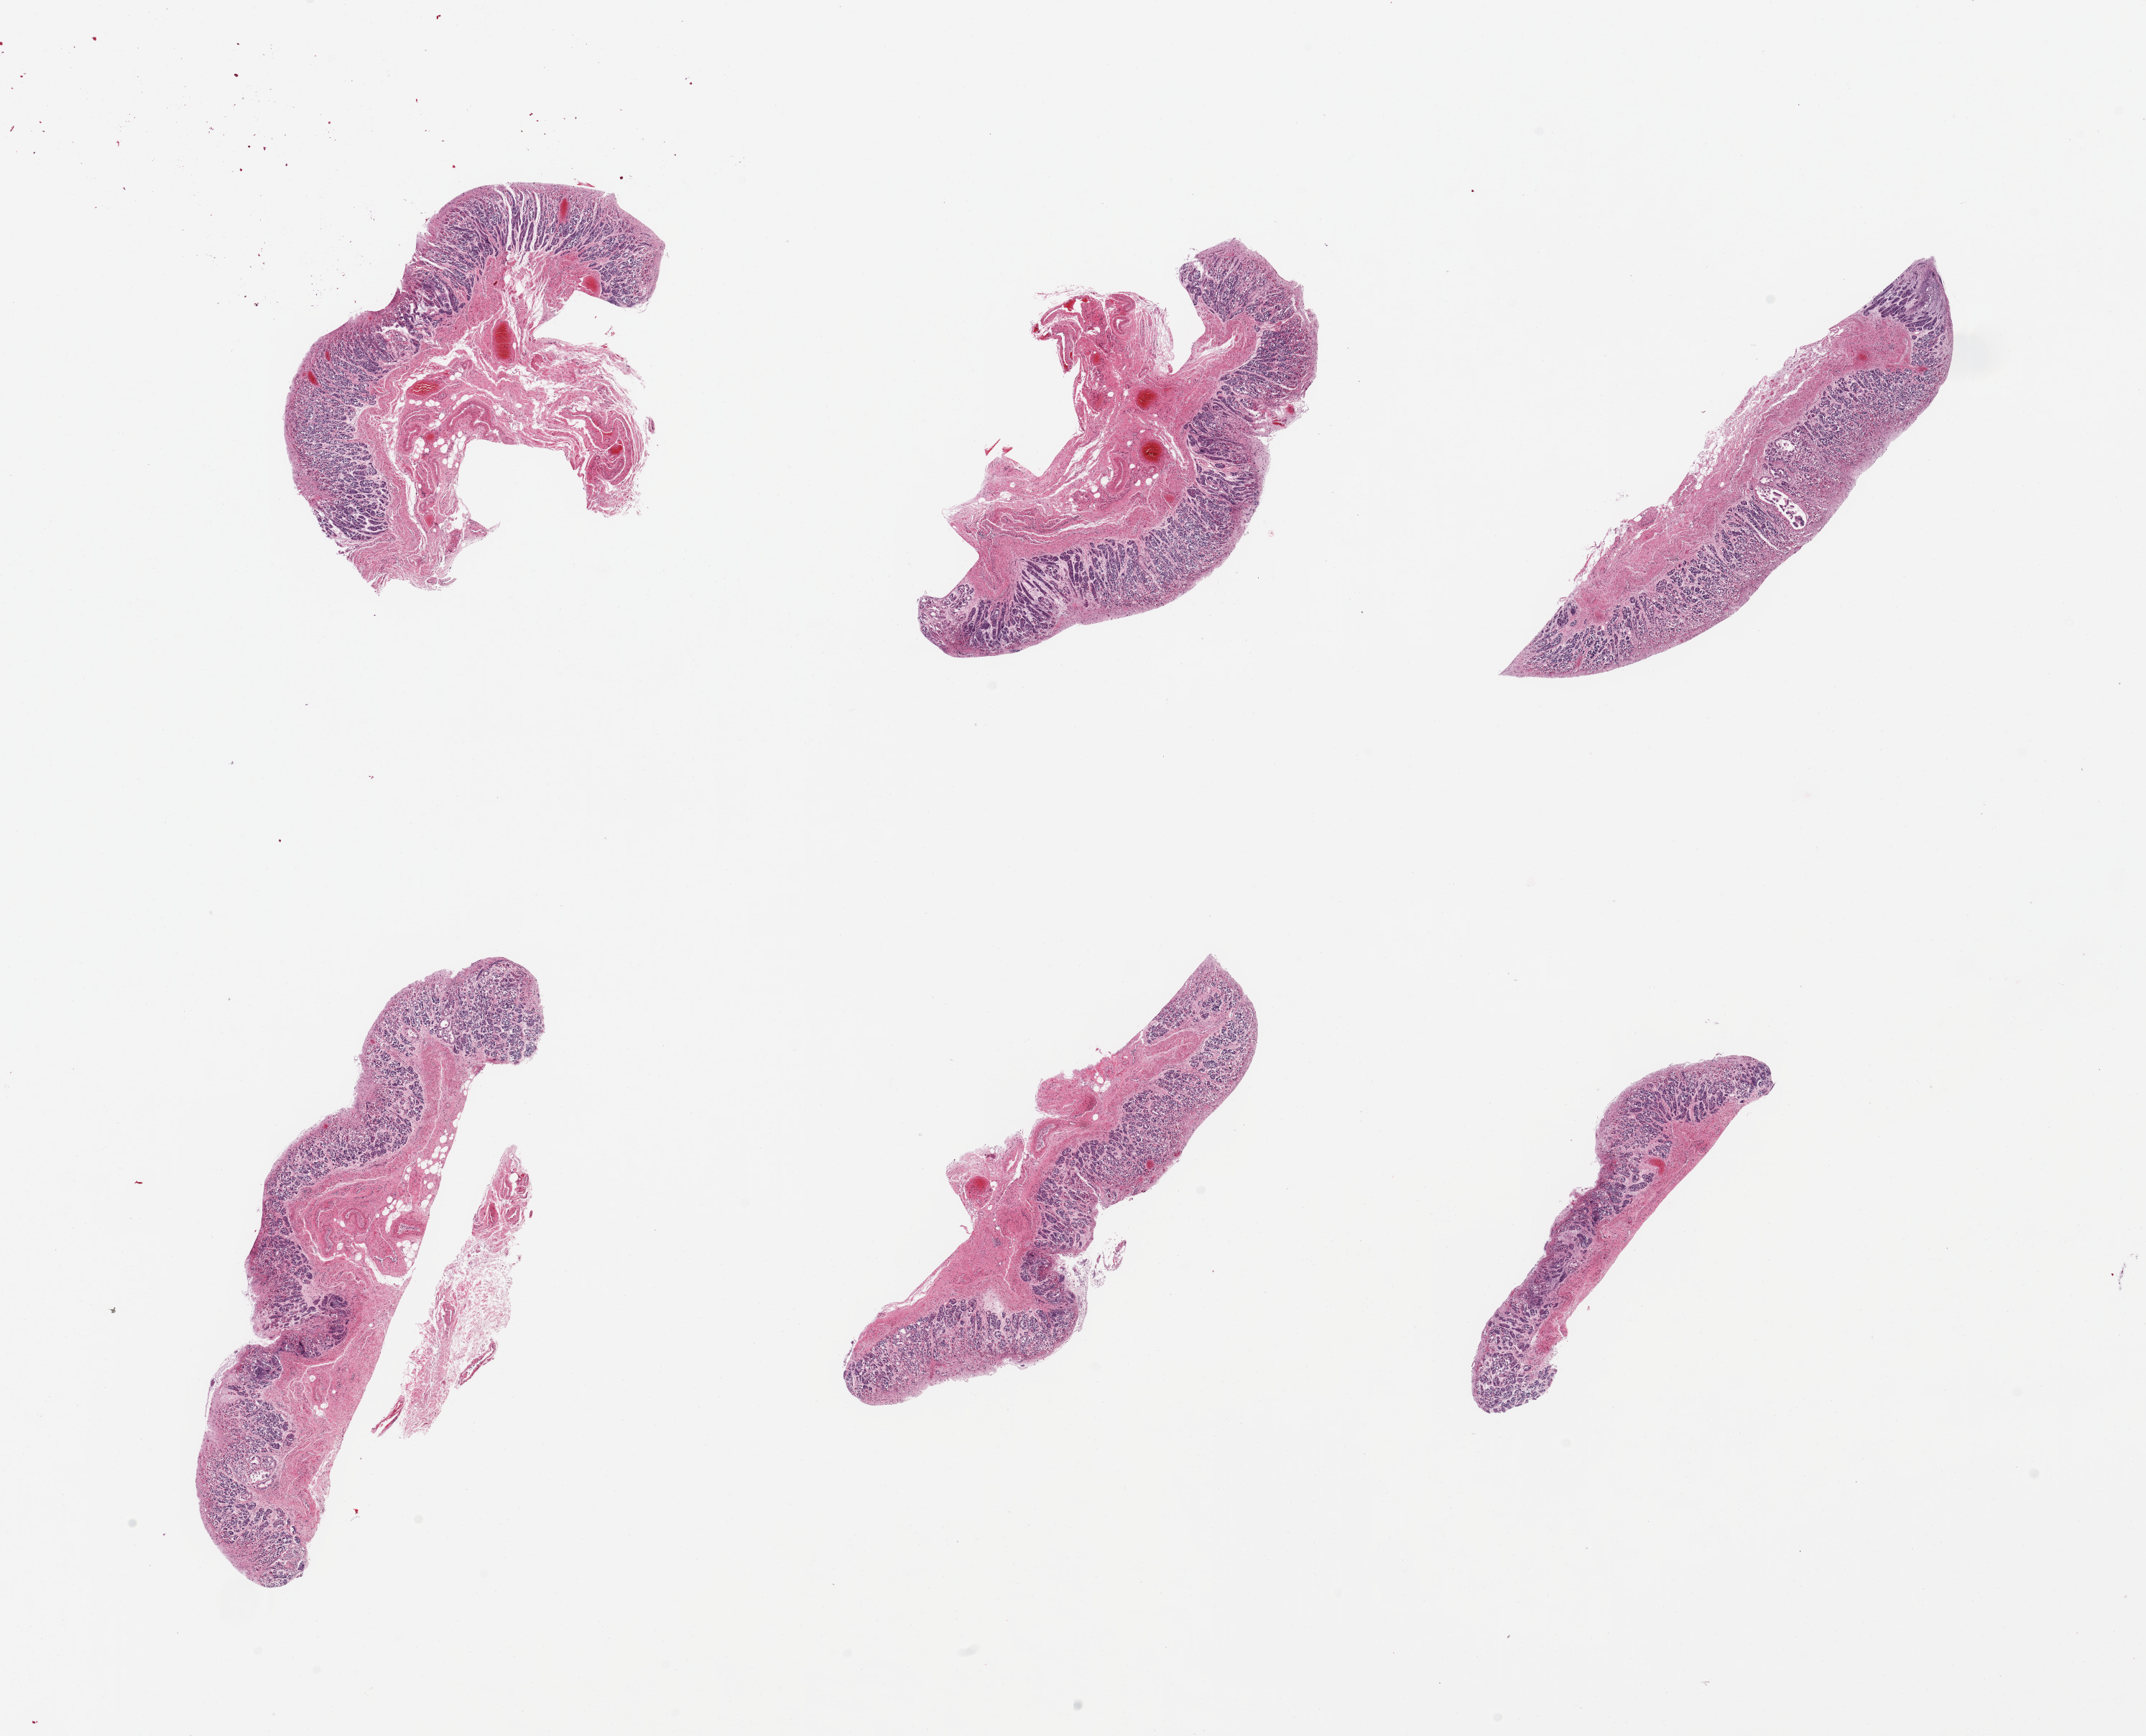
Hematoxylin and eosin (H&E) whole-slide image — a low-resolution overview of the entire scanned area, about 23.6 x 19.1 mm; PAXgene-fixed paraffin-embedded (PFPE) section; target tissue: esophageal mucous membrane; tissue donor sample. Donor: male.
• review note (as recorded): 6 pieces gastric cardiac mucosa; no squamous mucosa present